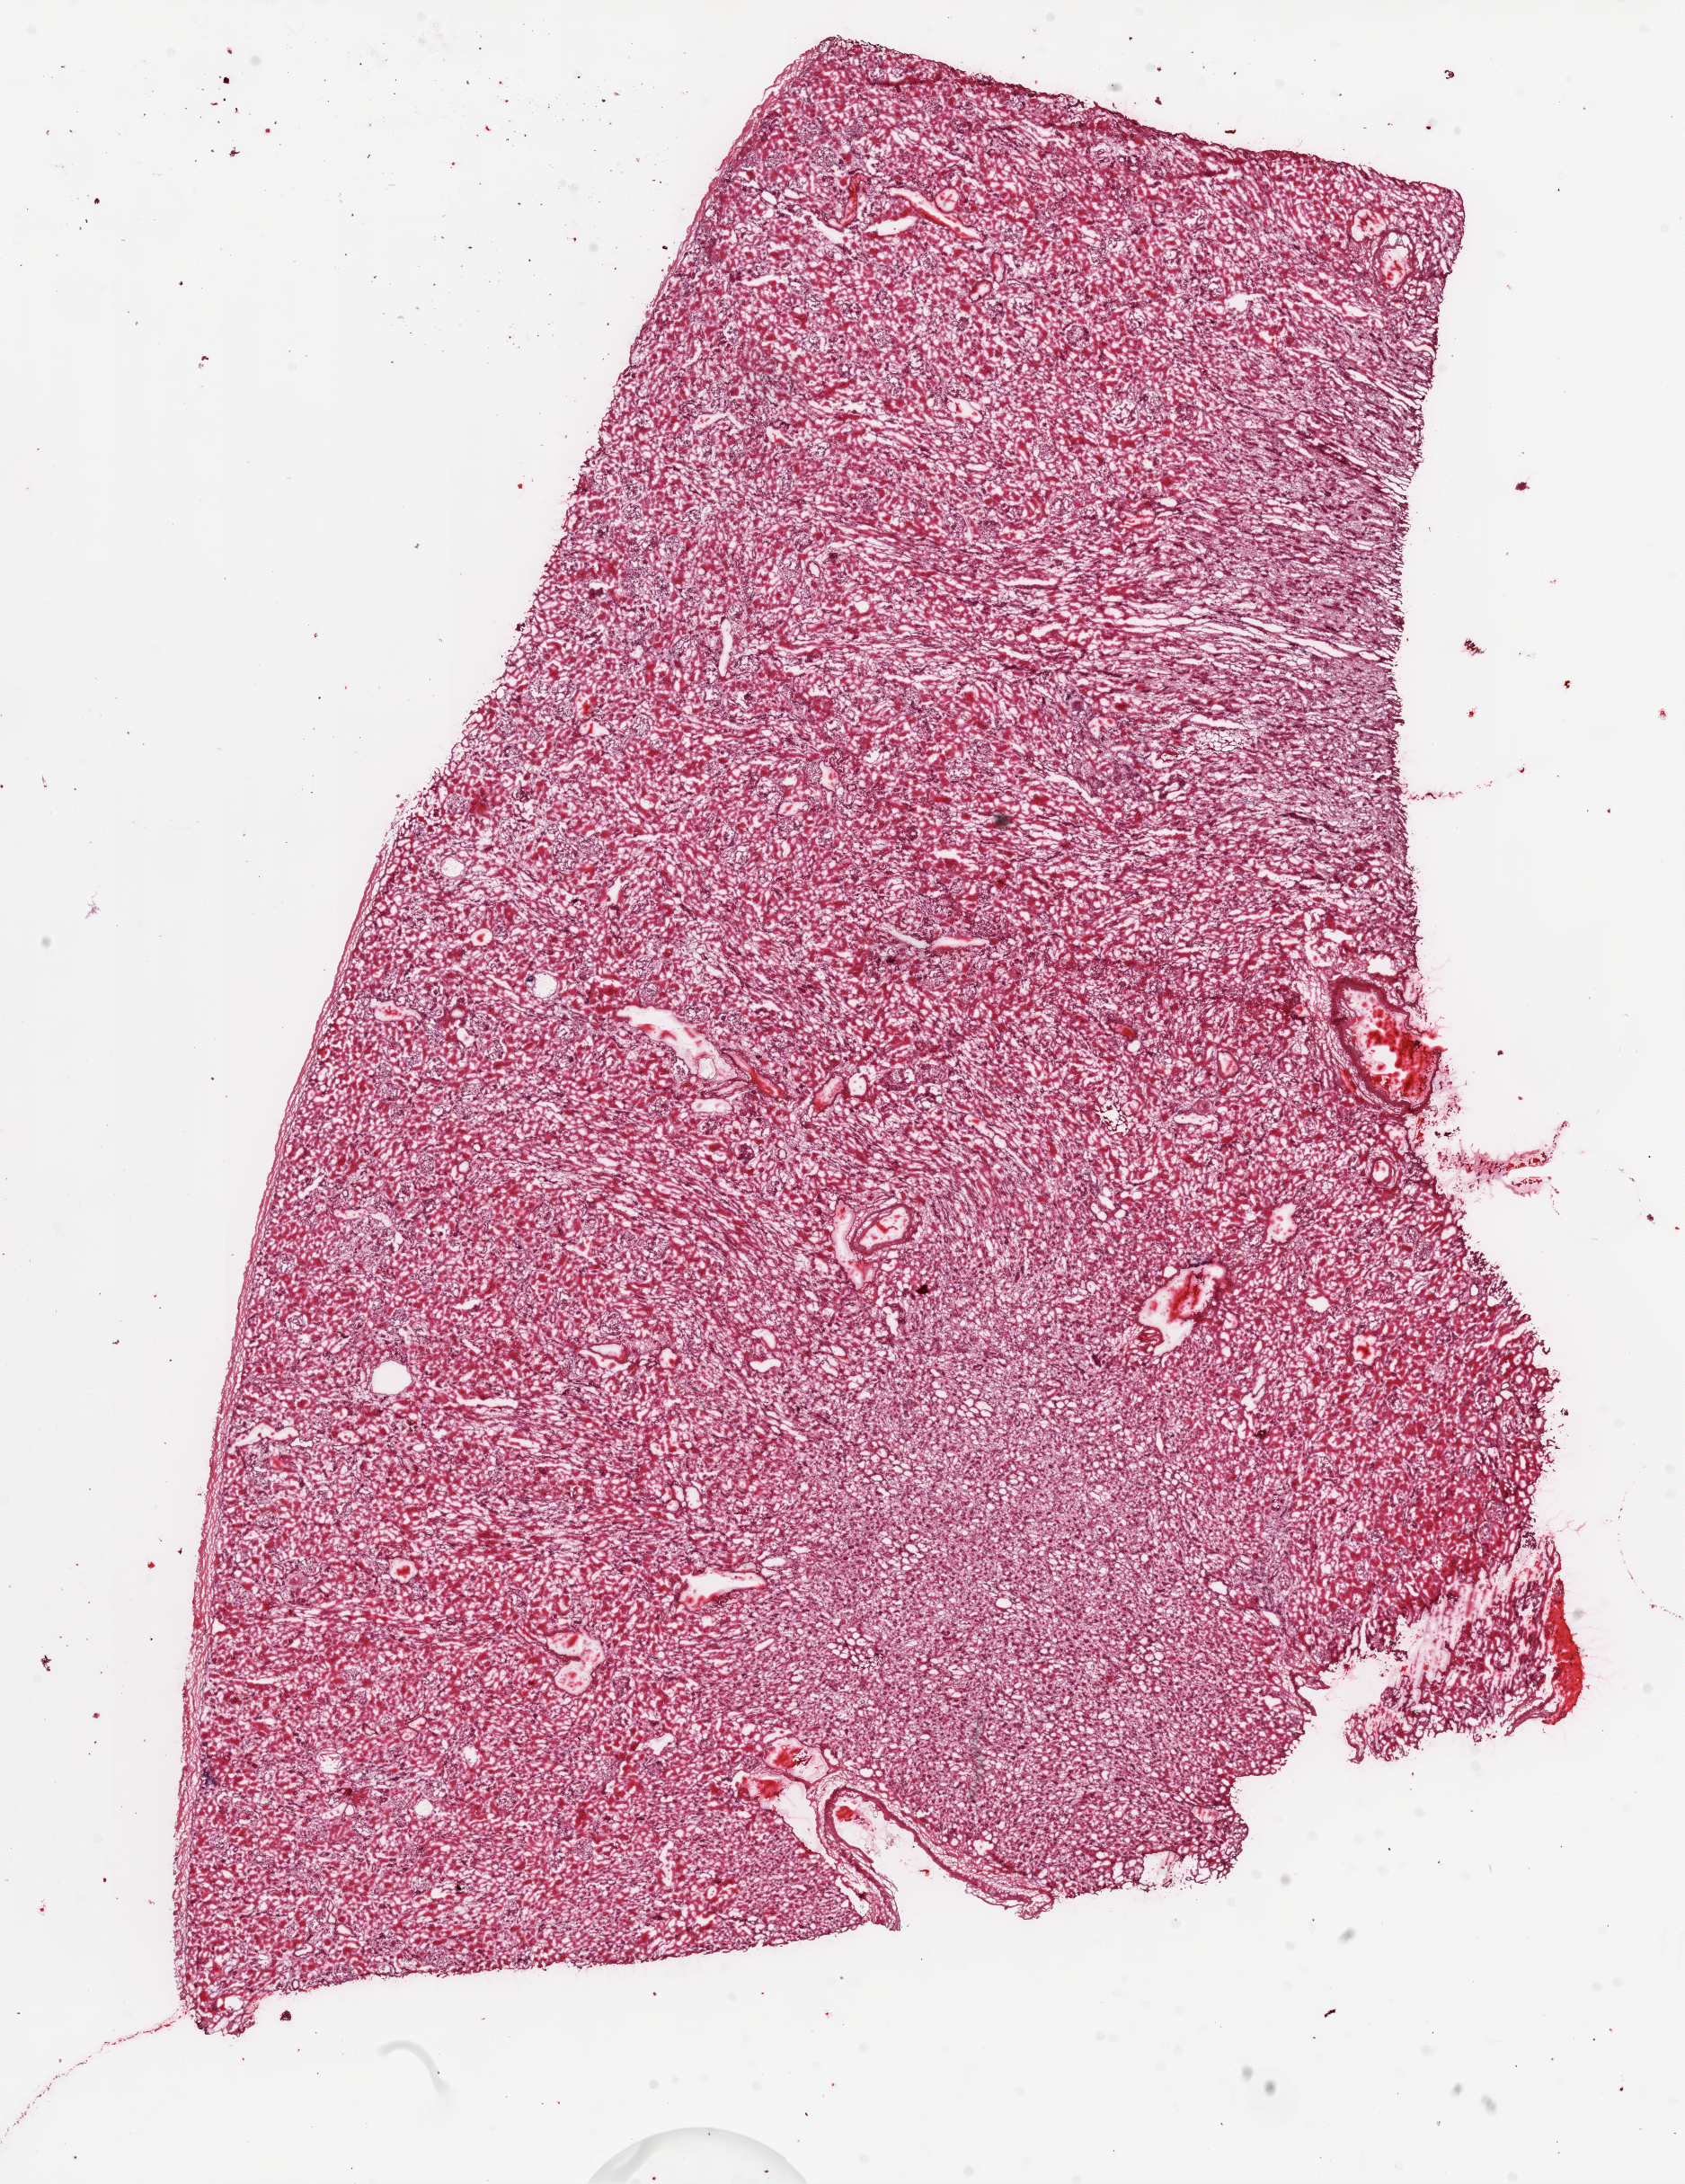
Digitized Hematoxylin and eosin (H&E) stained tissue section (whole slide), a low-resolution overview of the entire scanned area, about 15.0 x 19.5 mm. Frozen section from the top of the tissue portion. Sample: solid tissue normal (non-tumour tissue), kidney. Patient: female, age at initial diagnosis 62 years.
This section: solid tissue normal sample (biorepository sample class). Patient diagnosis: Clear cell adenocarcinoma, NOS.